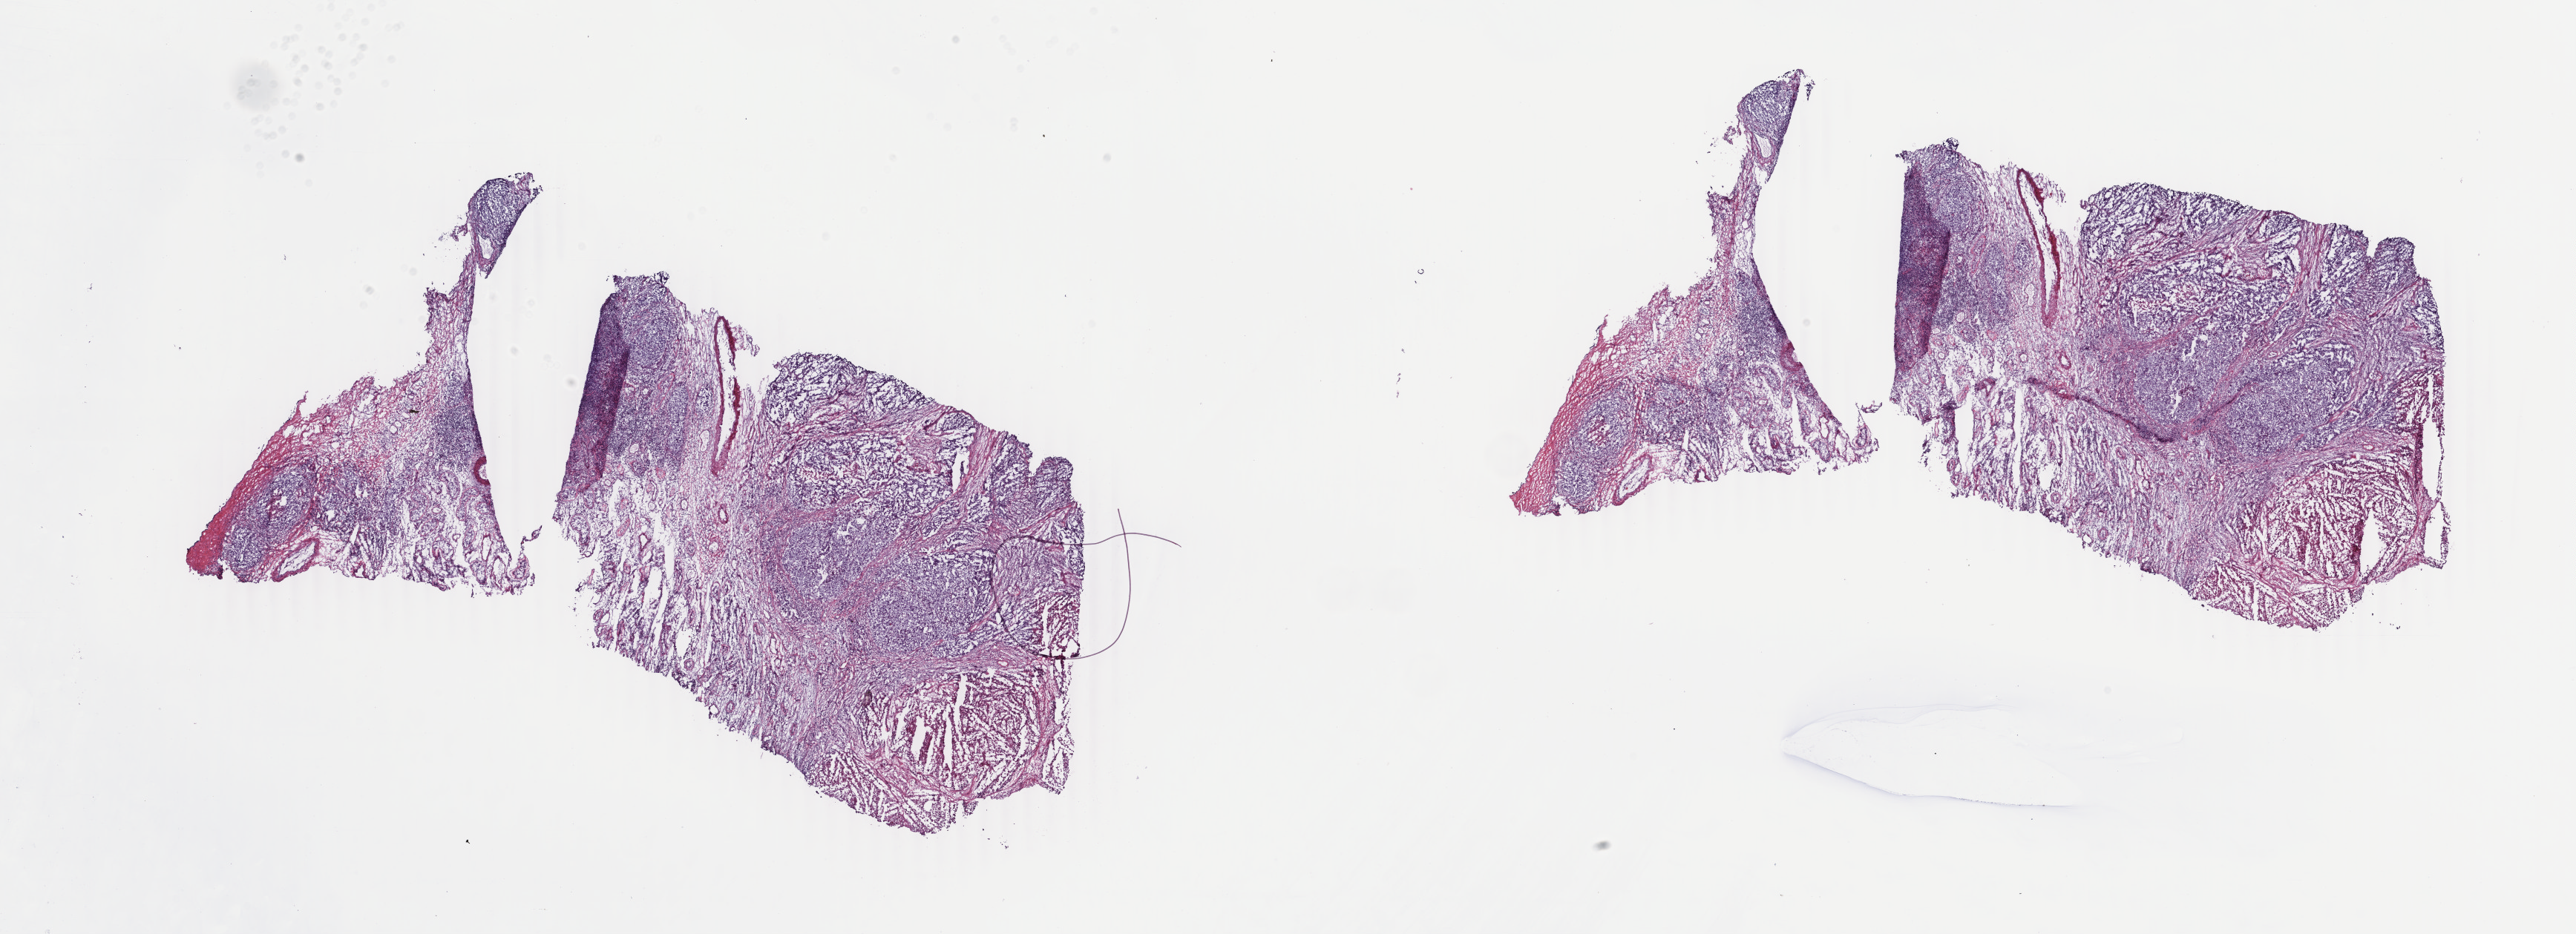
Digitized H&E tissue section (whole slide), whole scanned area (about 27.6 x 10.0 mm, from a 40x scan) shown as a low-resolution overview. Frozen section. Testis, primary tumour sample. Patient: male, age at initial diagnosis 24 years. Composition of this section per pathologist review: tumour cells 80%, tumour nuclei 90%, normal cells 0%, stromal cells 20%, necrosis 0%. Infiltration values recorded for this section: lymphocyte infiltration 0%, monocyte infiltration 0%, neutrophil infiltration 0%.
Pathologic diagnosis: Embryonal carcinoma, NOS. AJCC pathologic stage: IIA (7th edition).